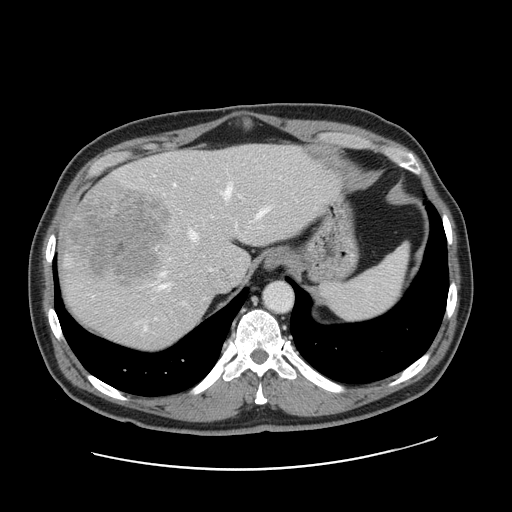
Contrast-enhanced abdominal CT, one axial slice. Slice 126 of 178 in the series (ordered by position). 120 kVp. Soft-tissue window (W 400 / L 40 HU). 2.5 mm slice thickness. 512 × 512 image matrix, field of view 403 × 403 mm. Male patient, age 63 years. From the clinical record (not read from this slice): diagnosis: colorectal cancer liver metastases, imaged before liver resection; multiple liver metastases: yes; largest metastasis: 8 cm; chemotherapy before resection: no.
Outlined on this slice (manually delineated by an expert):
- hepatic veins: bounding box <159,186,267,288> (left, top, right, bottom; pixels)
- liver: <60,144,340,349>
- planned liver remnant (the part of the liver to remain after resection): <149,145,340,279>
- portal vein (with intrahepatic branches): <155,183,213,319>
- liver metastasis: <67,179,171,290>